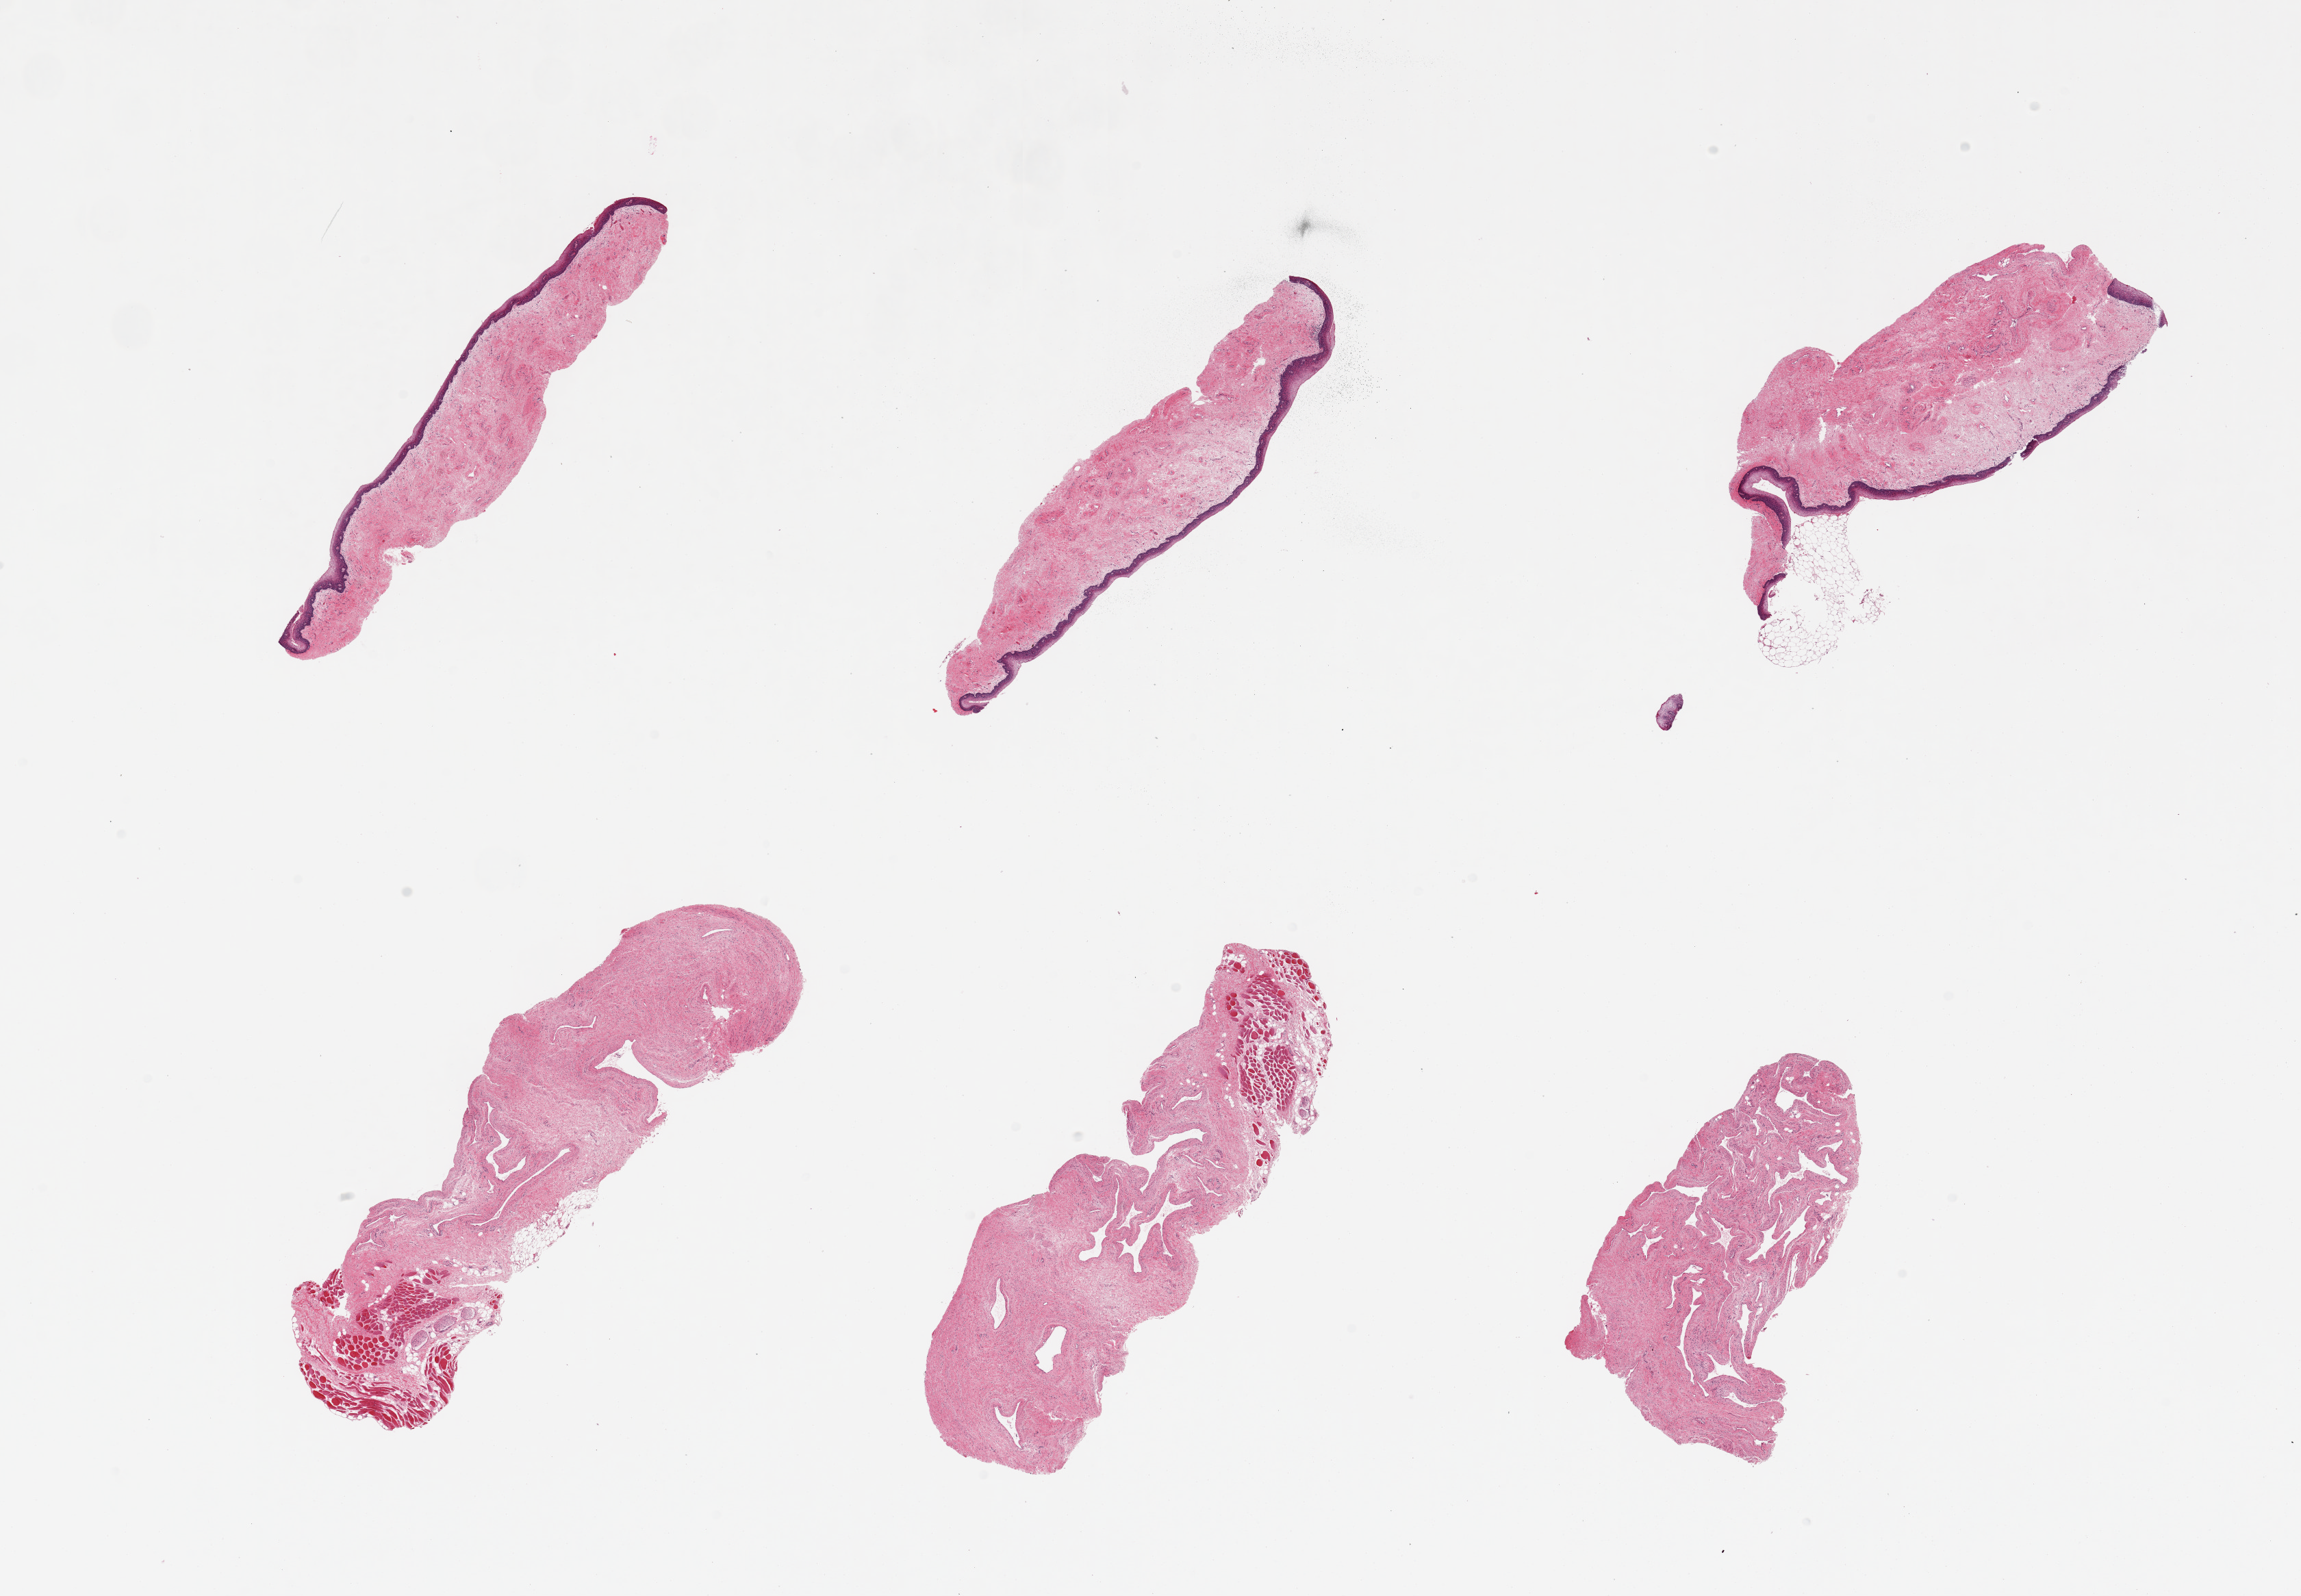
Whole-slide image, hematoxylin and eosin (H&E) stain, brightfield — low-resolution overview of the scanned area, about 26.6 x 18.4 mm; PAXgene-fixed paraffin-embedded (PFPE) section; target tissue: vagina; tissue donor sample. Female donor.
Pathologist's review note for this sample: 6 pieces, 3 with squamous epithelium.